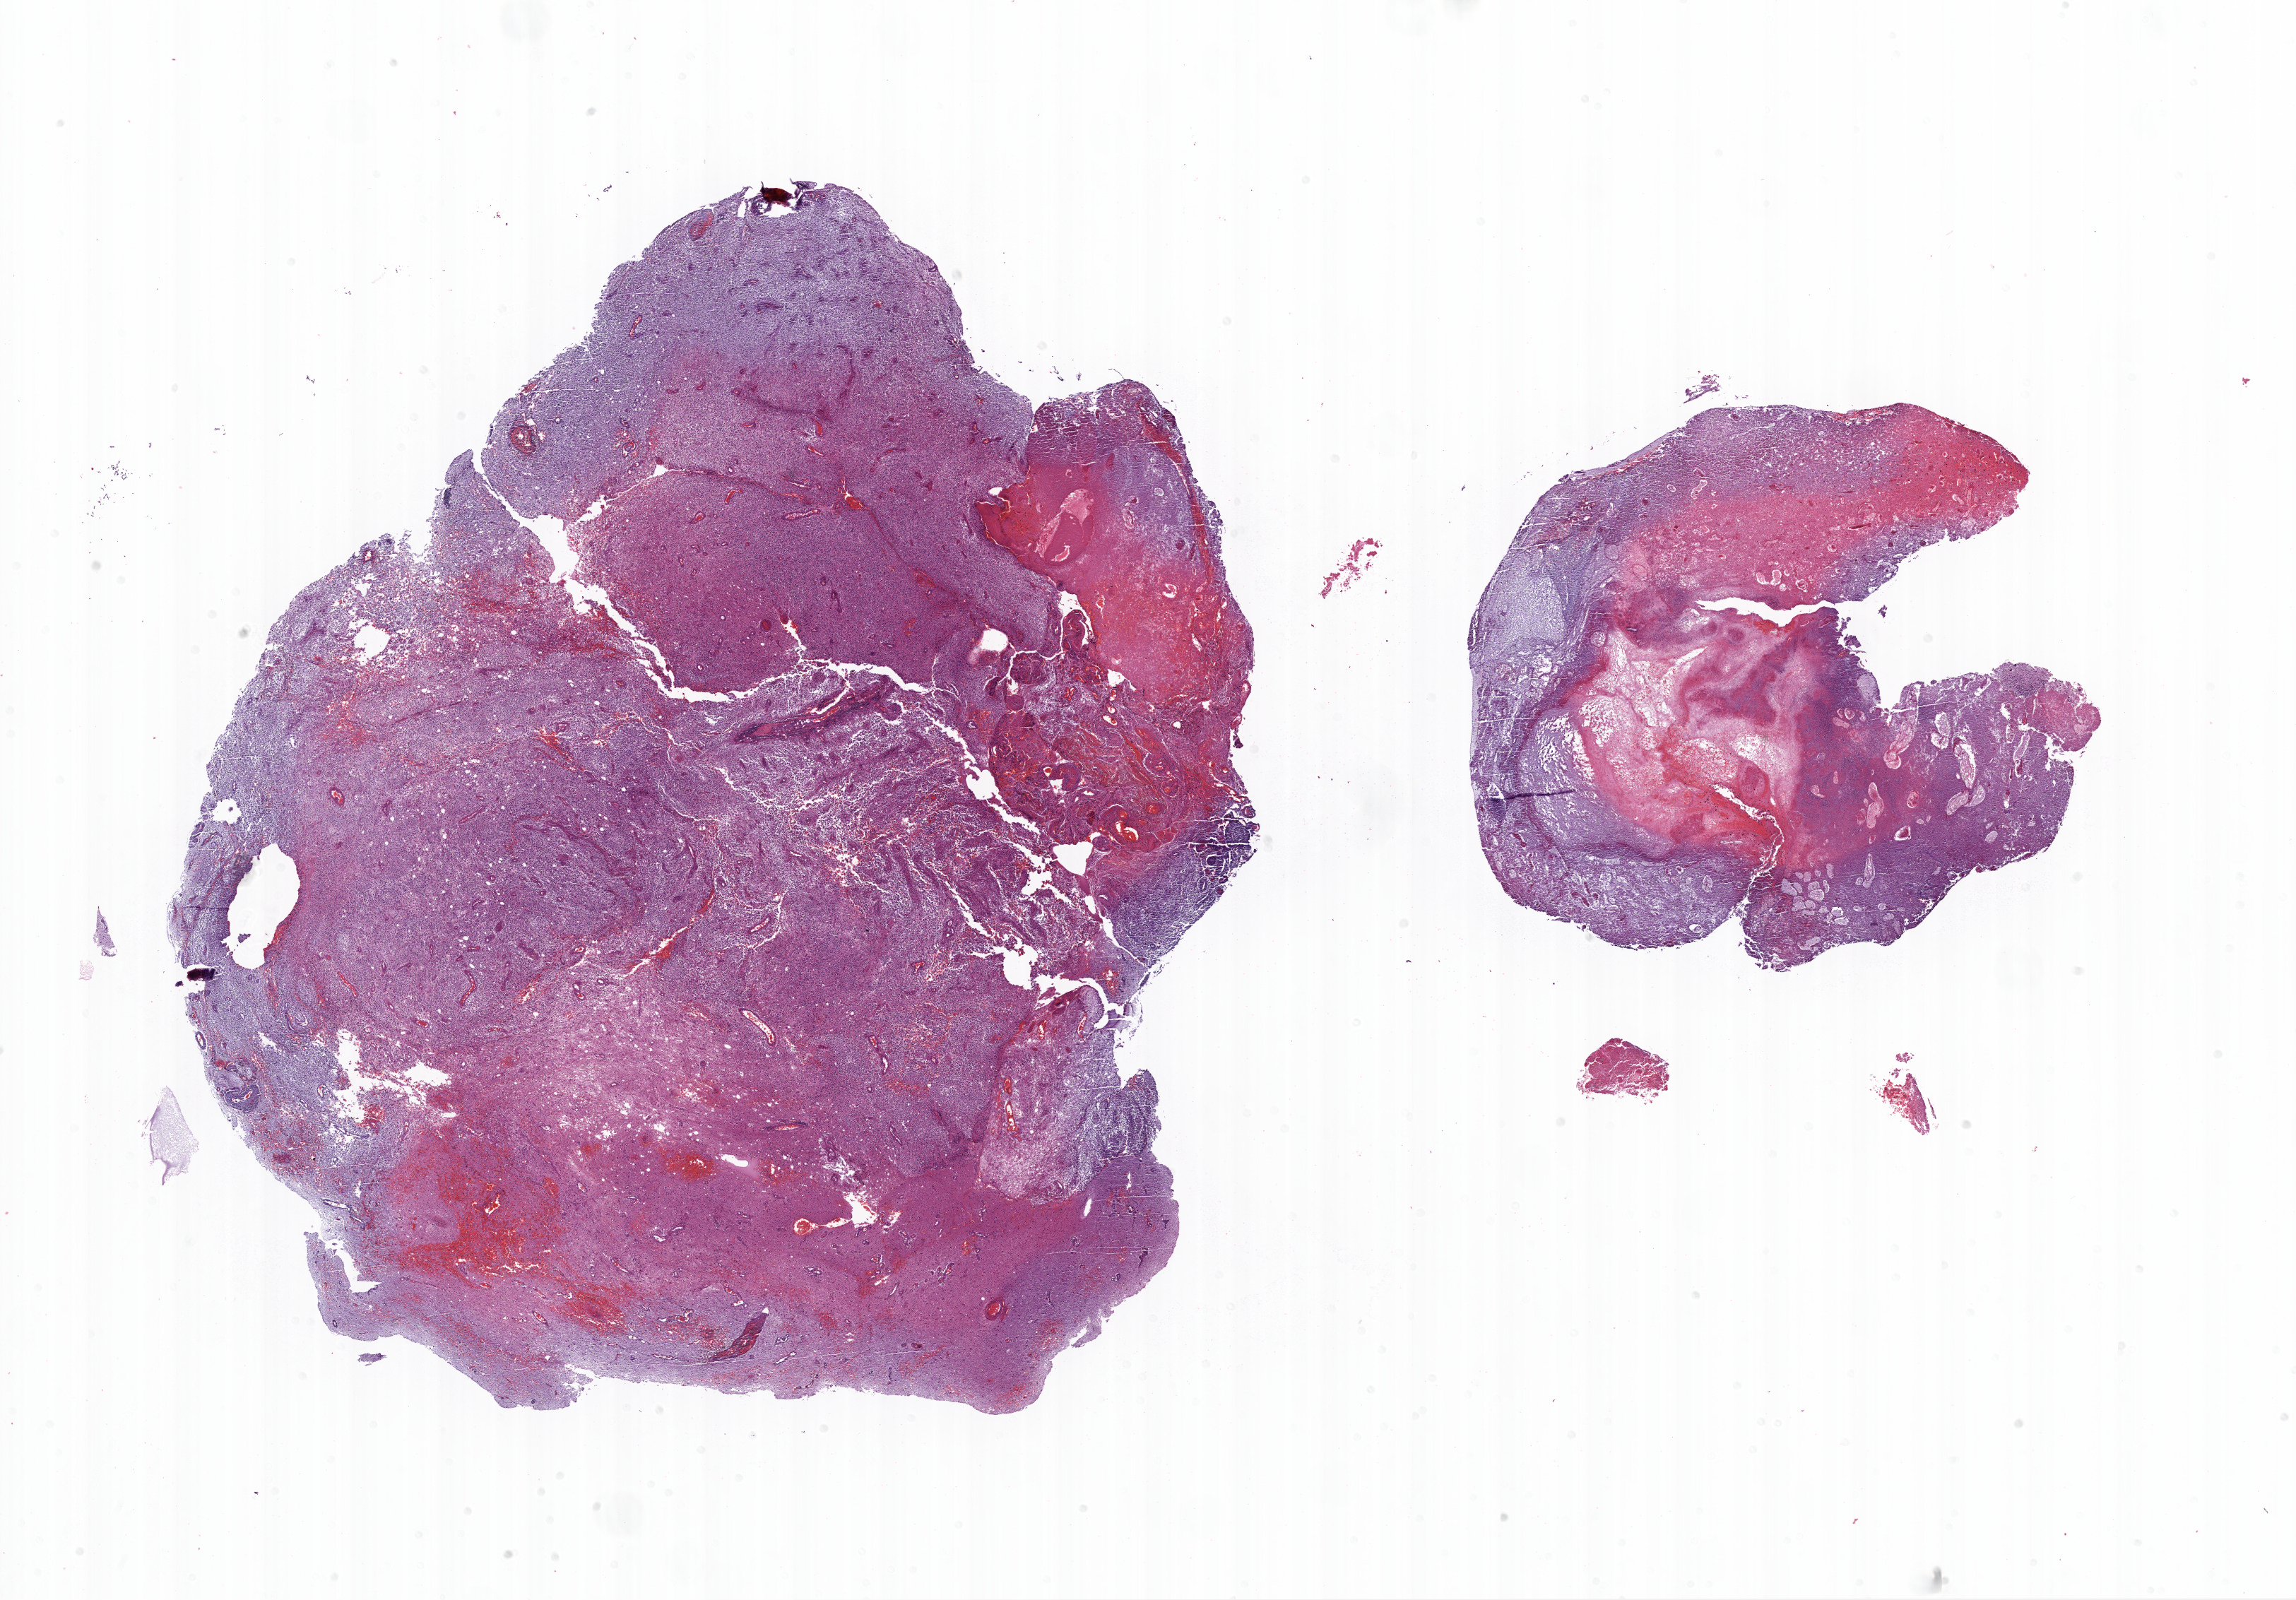
Whole-slide histology image, Hematoxylin and eosin (H&E) stained, shown as a low-resolution overview of the whole scanned area (about 26.1 x 18.2 mm, from a 20x scan), formalin-fixed paraffin-embedded (FFPE) diagnostic section, brain, primary tumour sample. Male patient; age at initial diagnosis 62 years.
Histologic diagnosis: Glioblastoma.